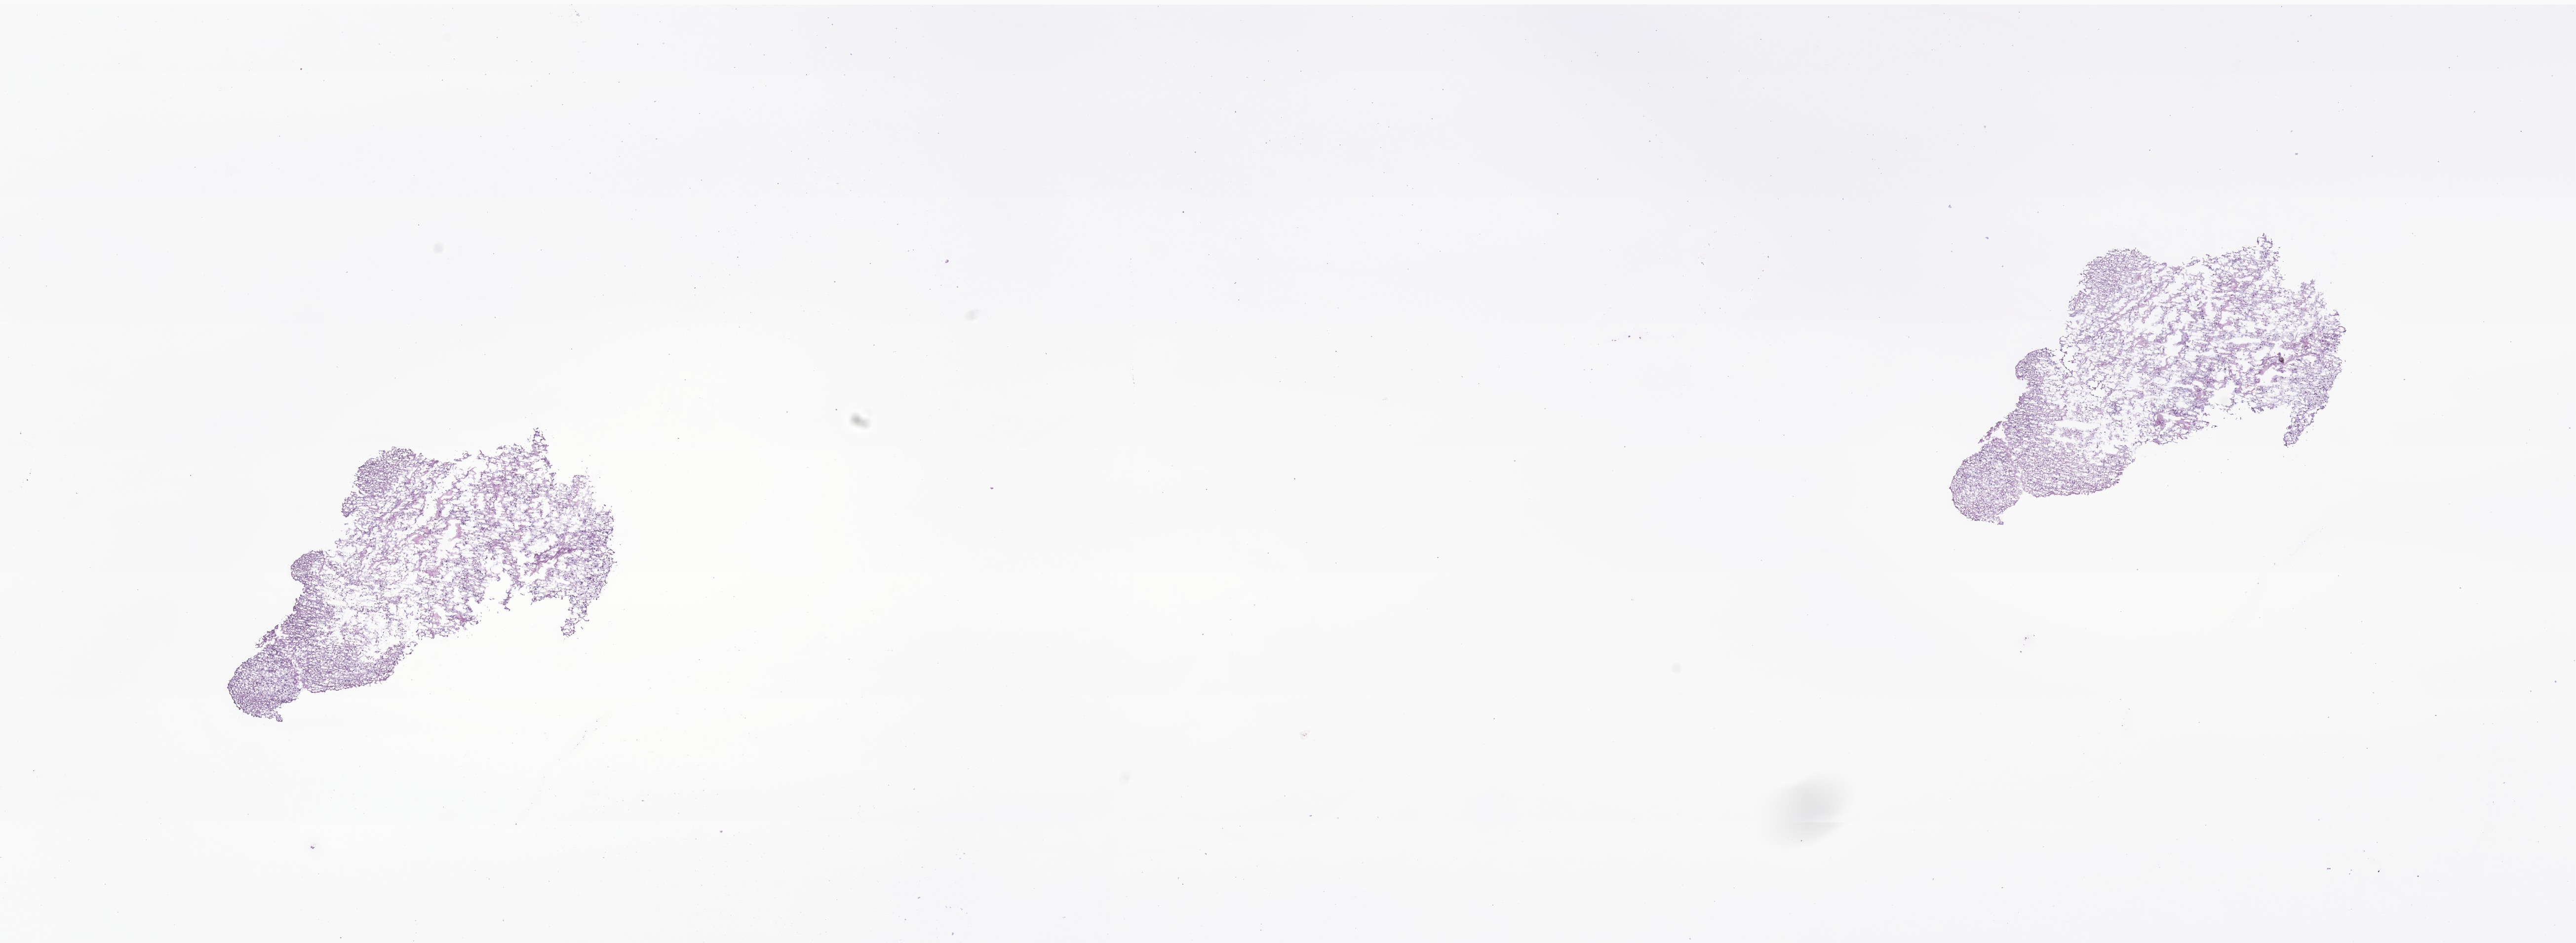
Whole-slide image, hematoxylin and eosin (H&E) stain of tumor tissue from the brain — low-resolution overview of the scanned area, about 22.0 x 8.1 mm, frozen section (OCT-embedded). Patient male; age 231 months.
Diagnosis (ICD-O-3 morphology term): Pilocytic astrocytoma.